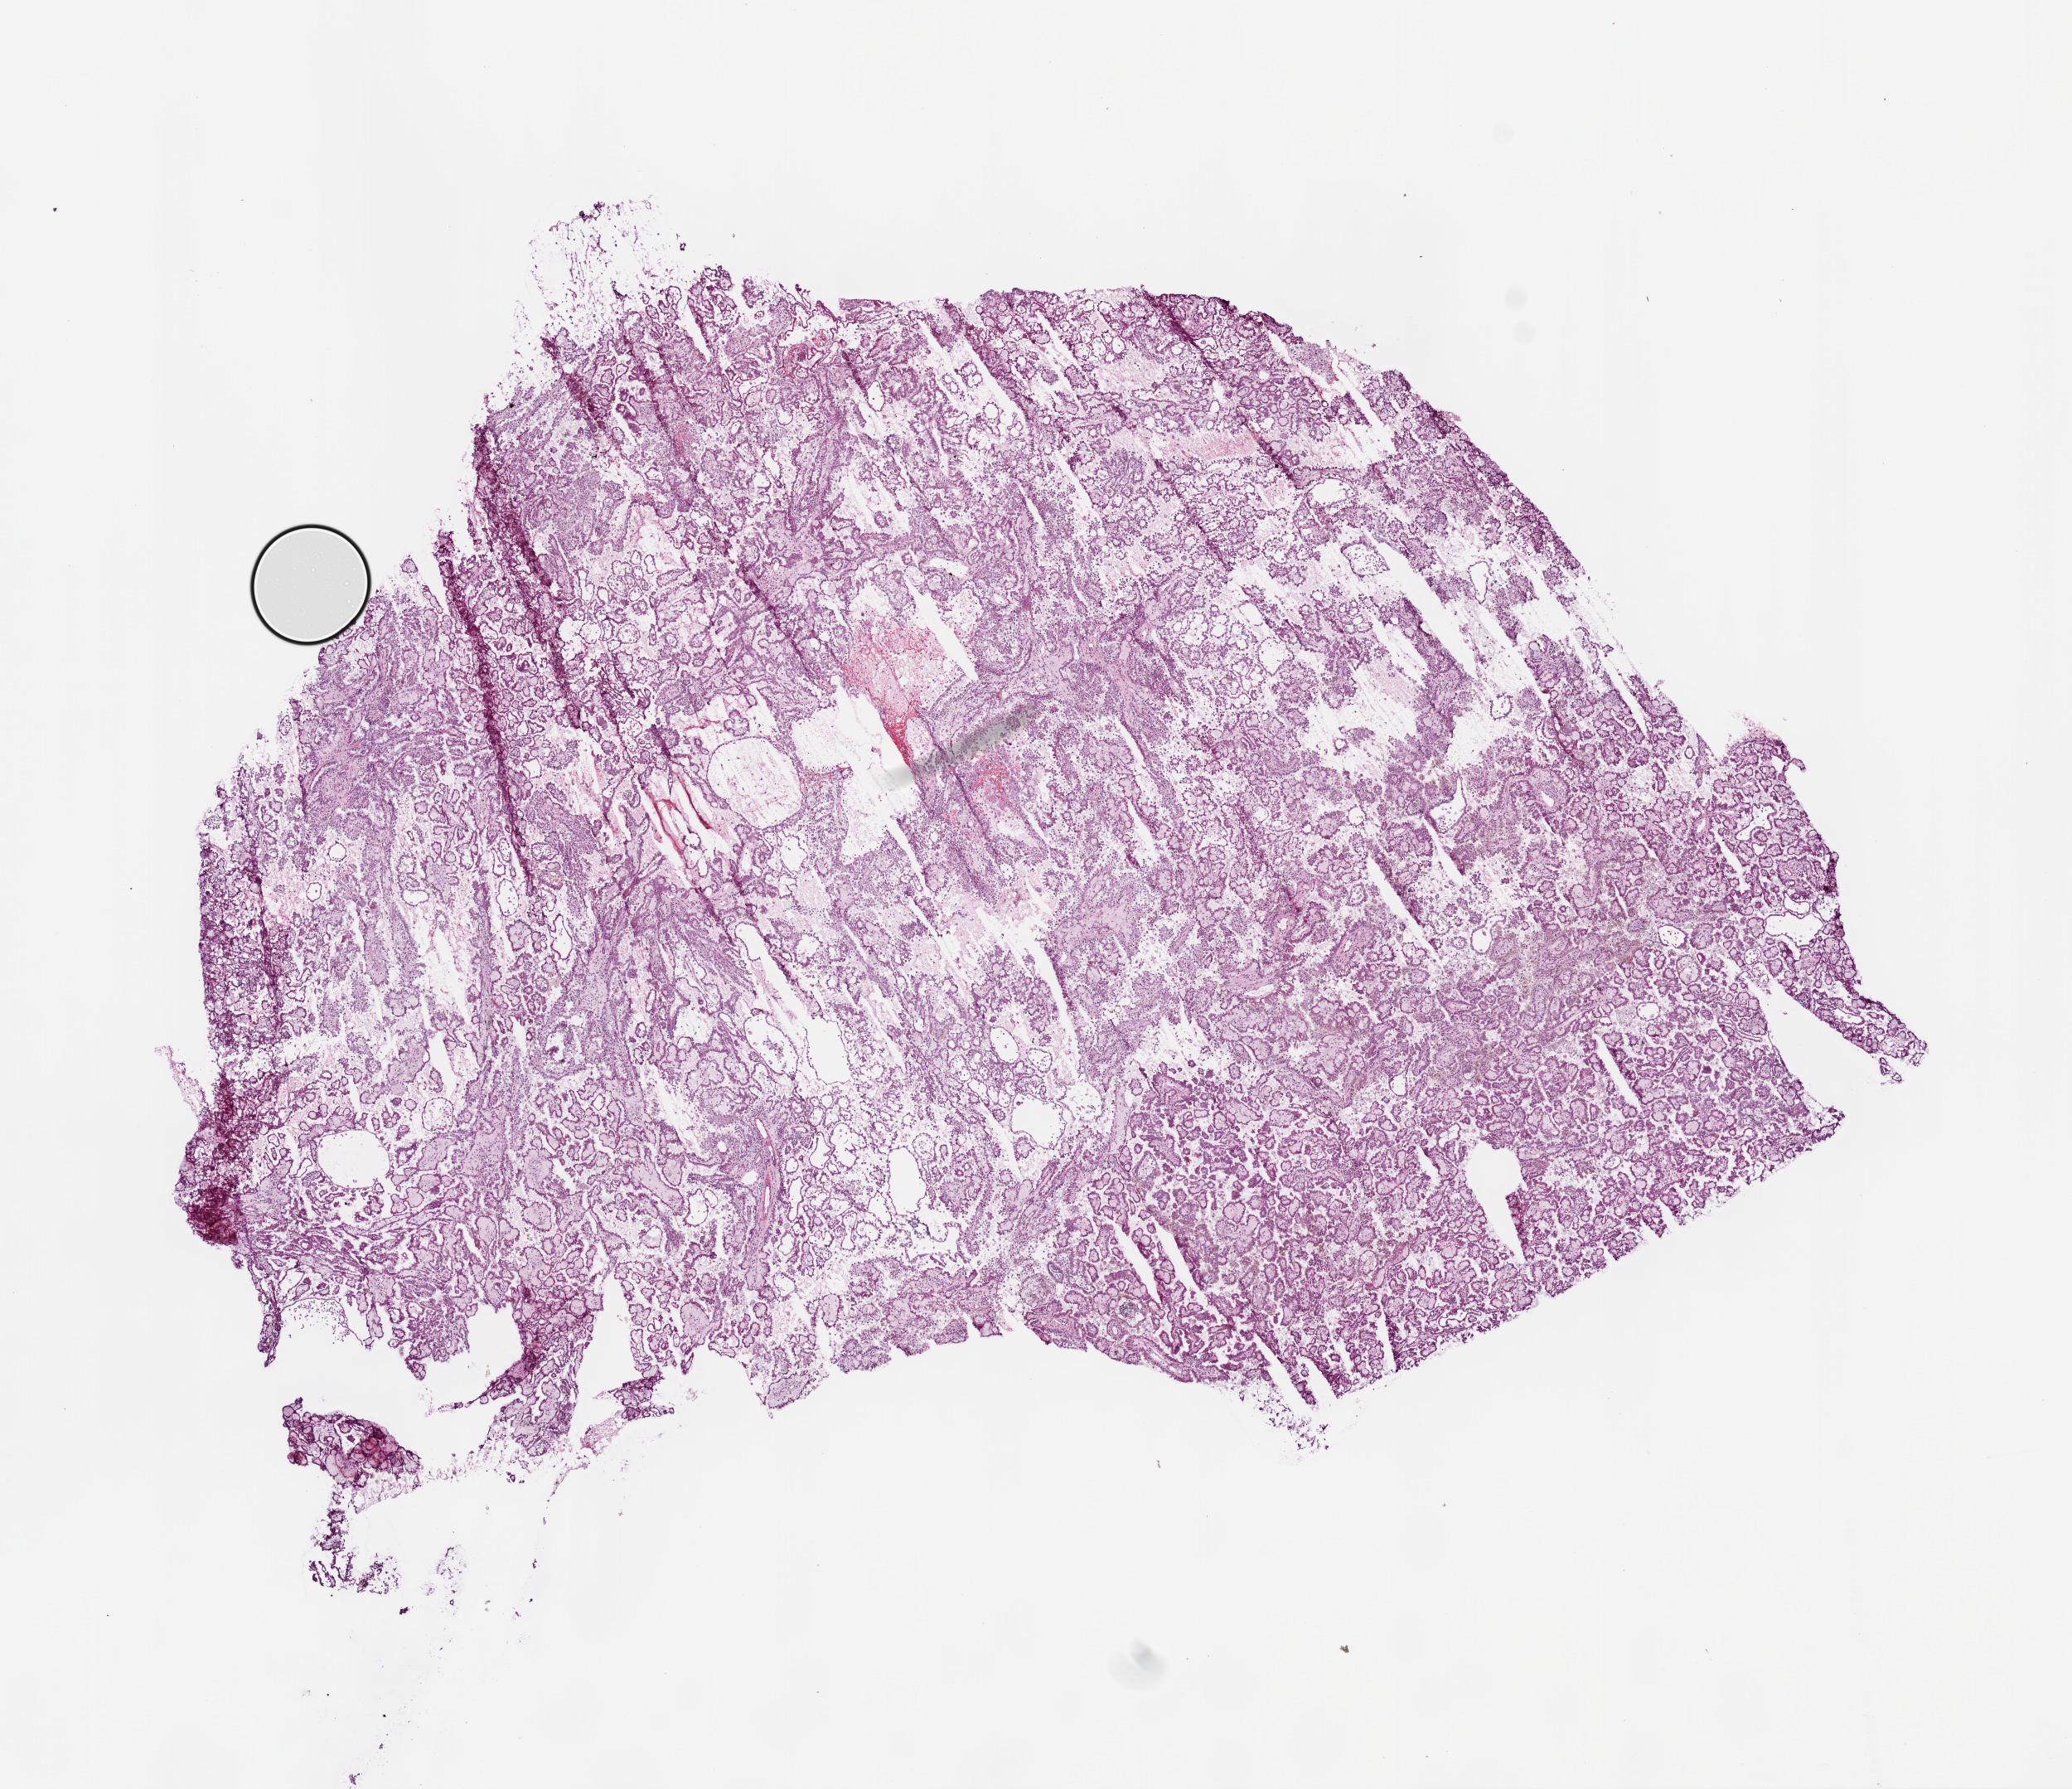
H&E whole-slide image, a low-resolution overview of the entire scanned area, about 10.0 x 8.7 mm (from a 20x scan). Frozen section from the bottom of the tissue portion. Primary tumour sample from the kidney. Male, age 51 years at initial diagnosis. Pathologist review of this section (percent, as recorded): tumour cells 87%, tumour nuclei 85%, normal cells 0%, stromal cells 10%, necrosis 3%.
Diagnosis: Papillary adenocarcinoma, NOS.